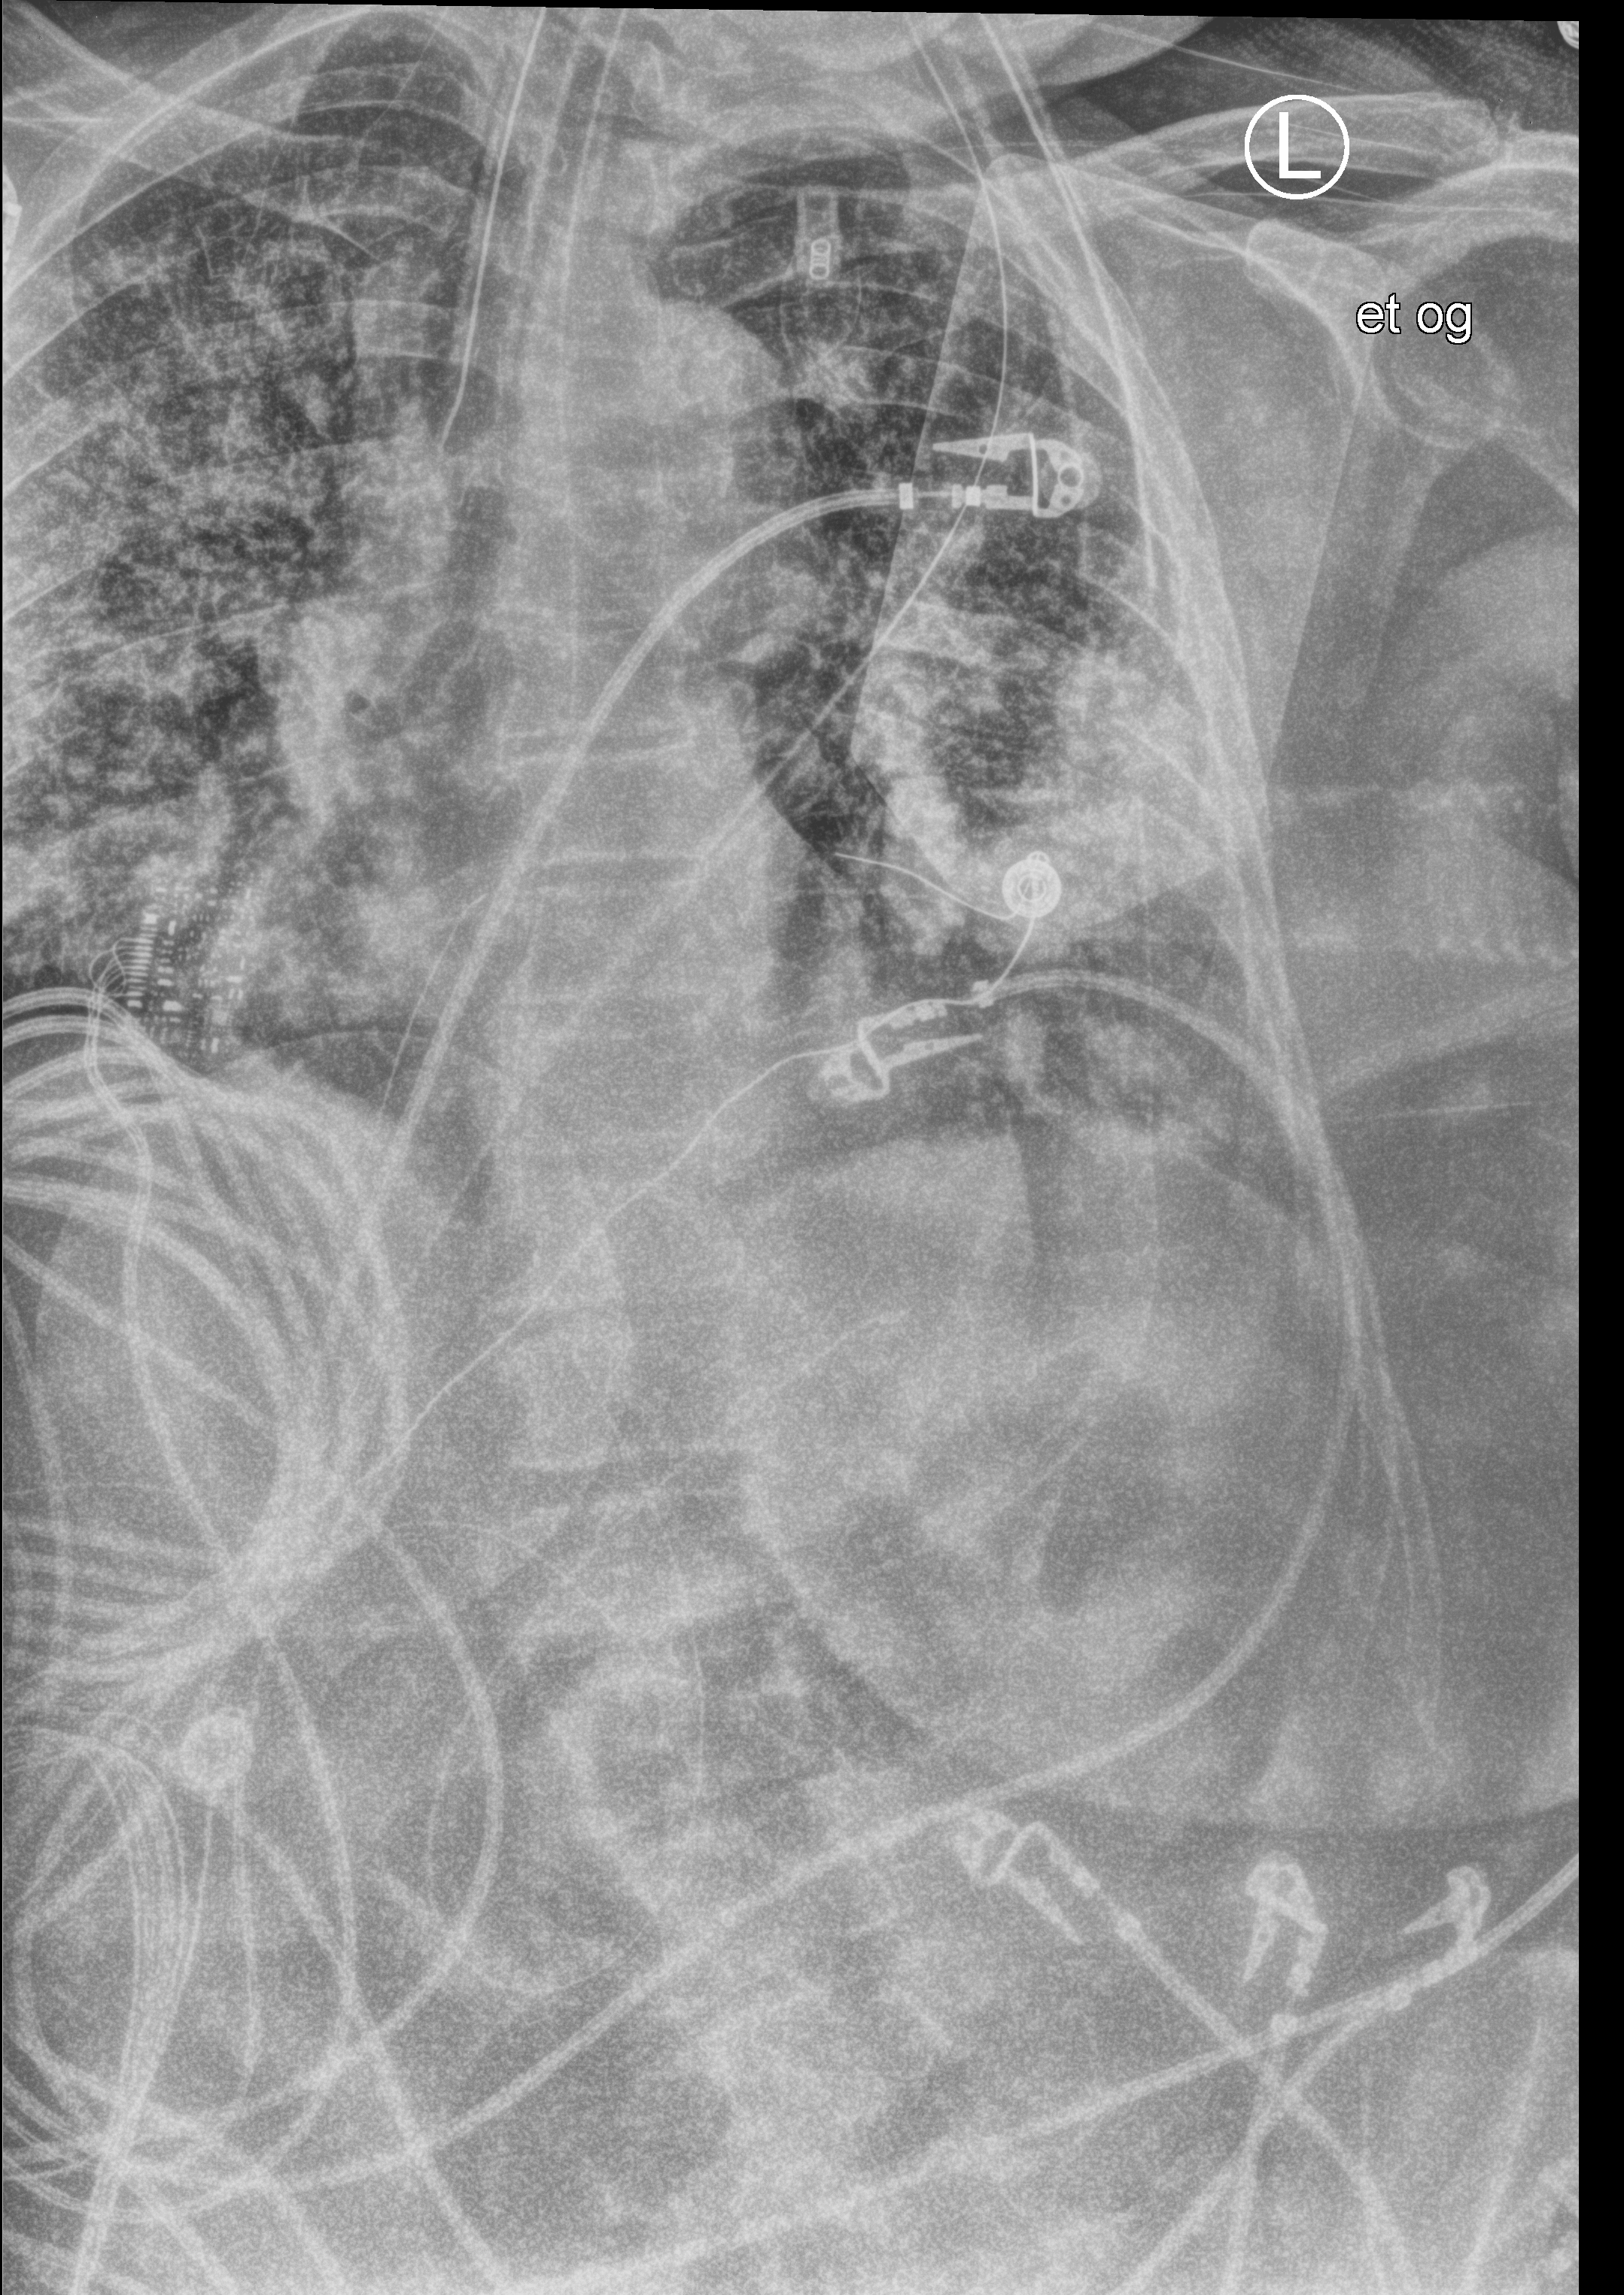
Chest X-ray (portable); anteroposterior (AP) projection. Patient hospitalised with COVID-19; female, aged 60–74 years.
Admission-level facts for this patient (not findings on this image; timing relative to this image not recorded): diabetes (admission record): no; mechanically ventilated during this hospital stay: yes; admitted to intensive care during this hospital stay: yes.